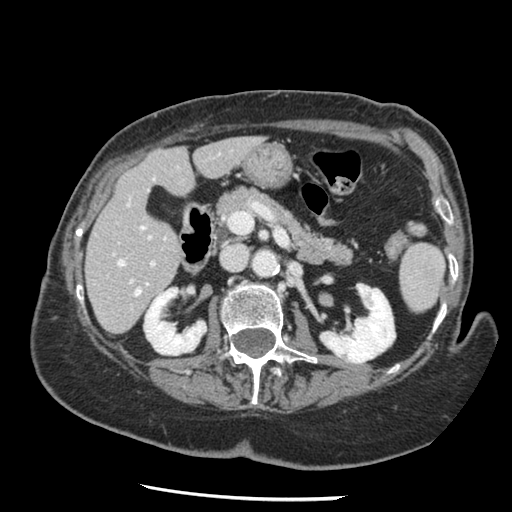
Contrast-enhanced abdominal CT, one axial slice. Position 62 of 148 along the scan axis. Reconstruction kernel STANDARD. Intravenous contrast given. Soft-tissue window (W 400 / L 40 HU). 512 × 512 image matrix, field of view 330 × 330 mm. Female patient, age 85 years. From the clinical record (not read from this slice): diagnosis: colorectal cancer liver metastases, imaged before liver resection; multiple liver metastases: no; largest metastasis: 0.9 cm; chemotherapy before resection: yes.
Outlined on this slice (manually delineated by an expert):
- hepatic veins: bounding box [x1, y1, x2, y2] px = [118, 226, 147, 295]
- liver: [86, 137, 260, 333]
- planned liver remnant (the part of the liver to remain after resection): [86, 137, 260, 321]
- portal vein (with intrahepatic branches): [151, 262, 155, 266]